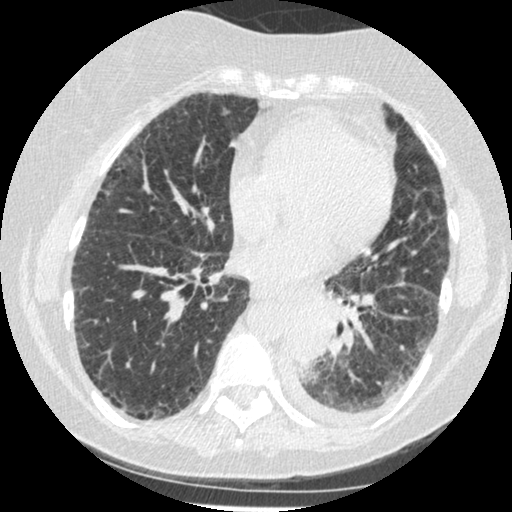
Chest CT (low-dose screening protocol), one axial image. Third annual screen. Lung window (W 1500 / L -600 HU). Slice 250 of 341 in the series. 512 × 512 image matrix. Female participant, aged 60 years at enrolment. Former smoker at enrolment.
Lesion marked by an expert reader, bounding box <277,302,343,376> (left, top, right, bottom; pixels). Screening reader's record for this exam (one nodule recorded; not confirmed to be the boxed lesion): non-calcified nodule or mass ≥4 mm, left lower lobe, 54 × 38 mm, smooth margins, soft tissue attenuation, pre-existing on the prior screen: yes; interval growth: yes. Official screen result: positive, other. Participant outcome: lung cancer diagnosed 15 days after this screen — small cell carcinoma, NOS, left lower lobe, undifferentiated (G4), stage IV (AJCC 6th edition), 69 mm at pathology.